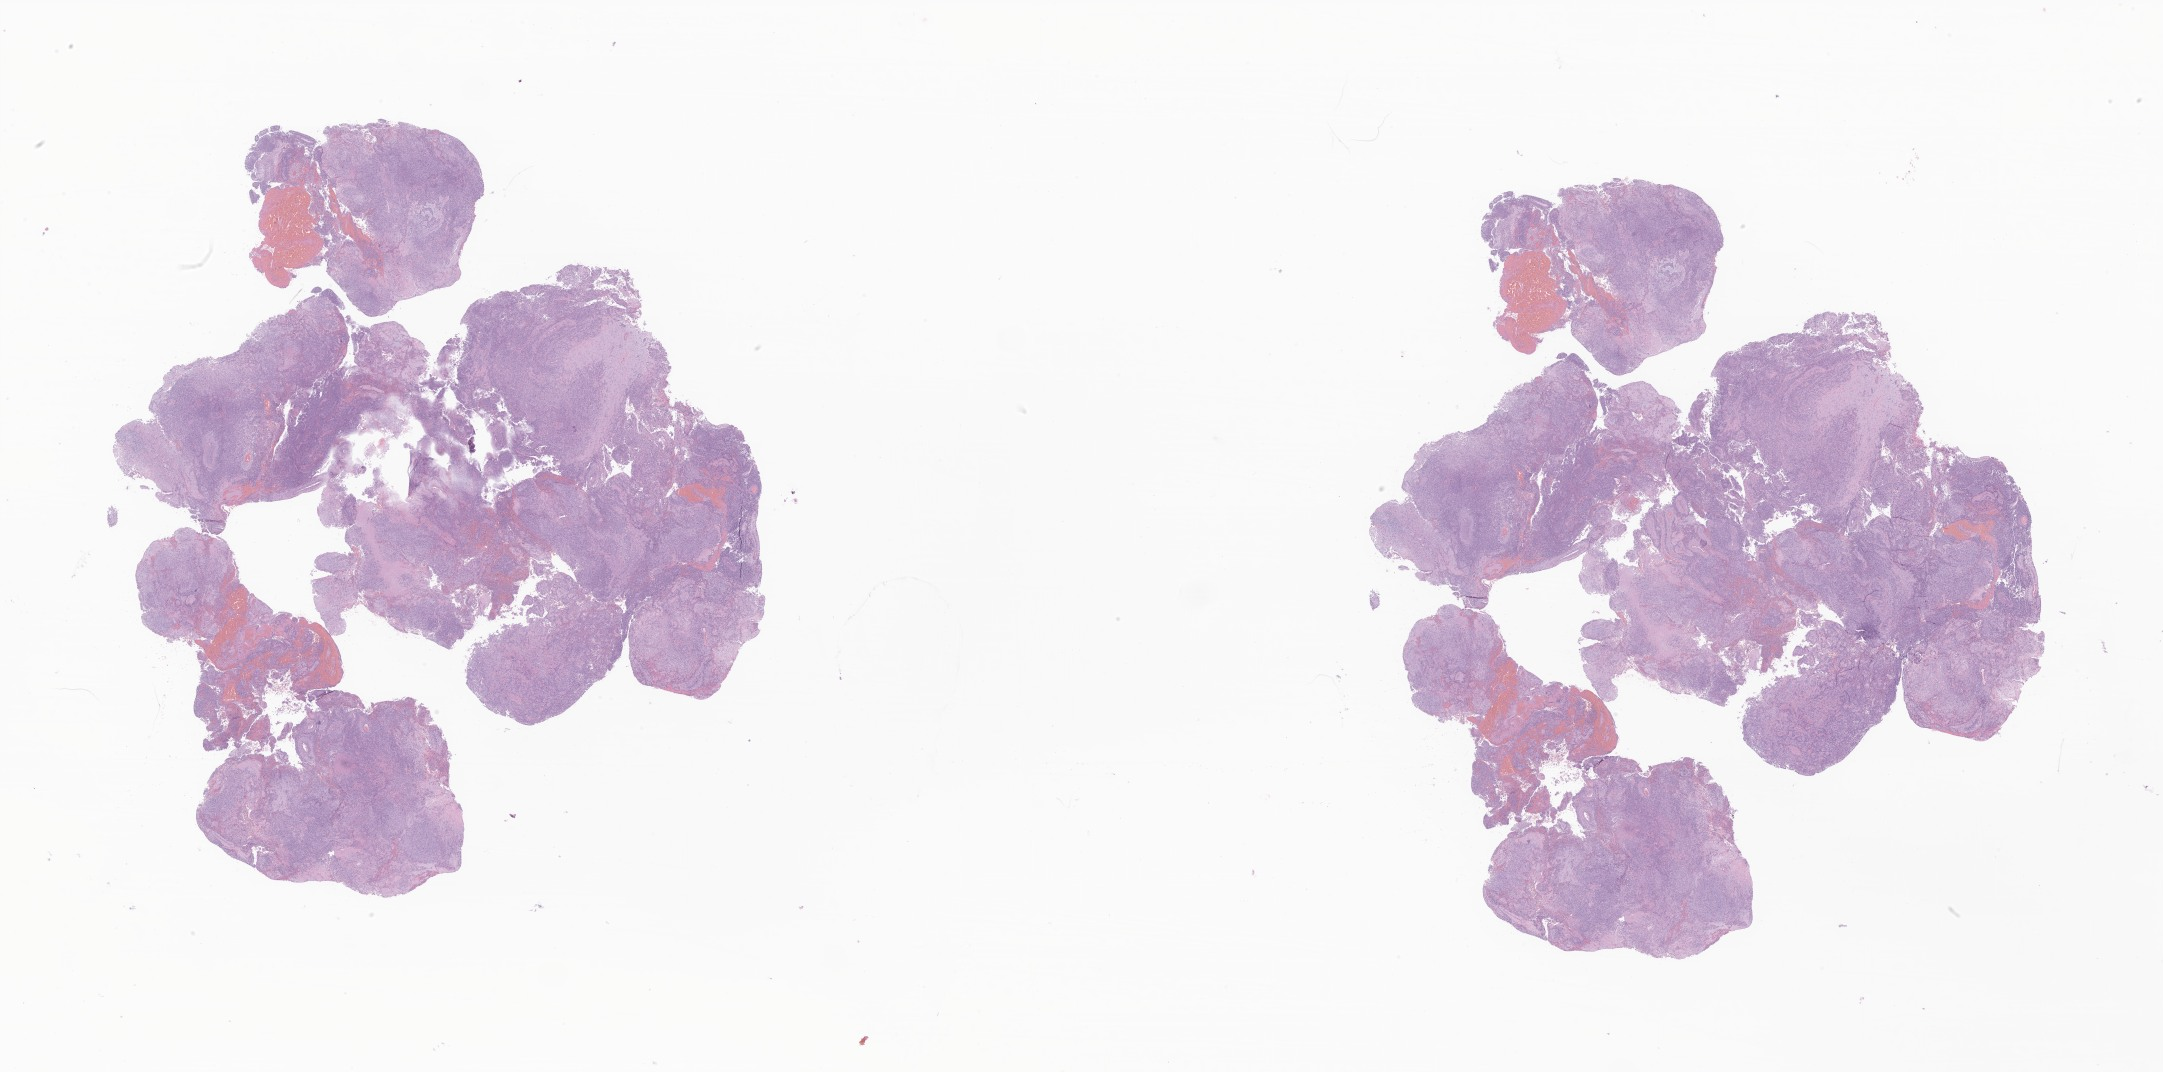
Haematoxylin and eosin whole-slide image of tumor tissue from the brain, whole scanned area (about 36.5 x 18.1 mm) shown as a low-resolution overview. FFPE section. Patient: female, age 71 months (5 years 11 months).
Recorded diagnosis: Neoplasm, uncertain whether benign or malignant.